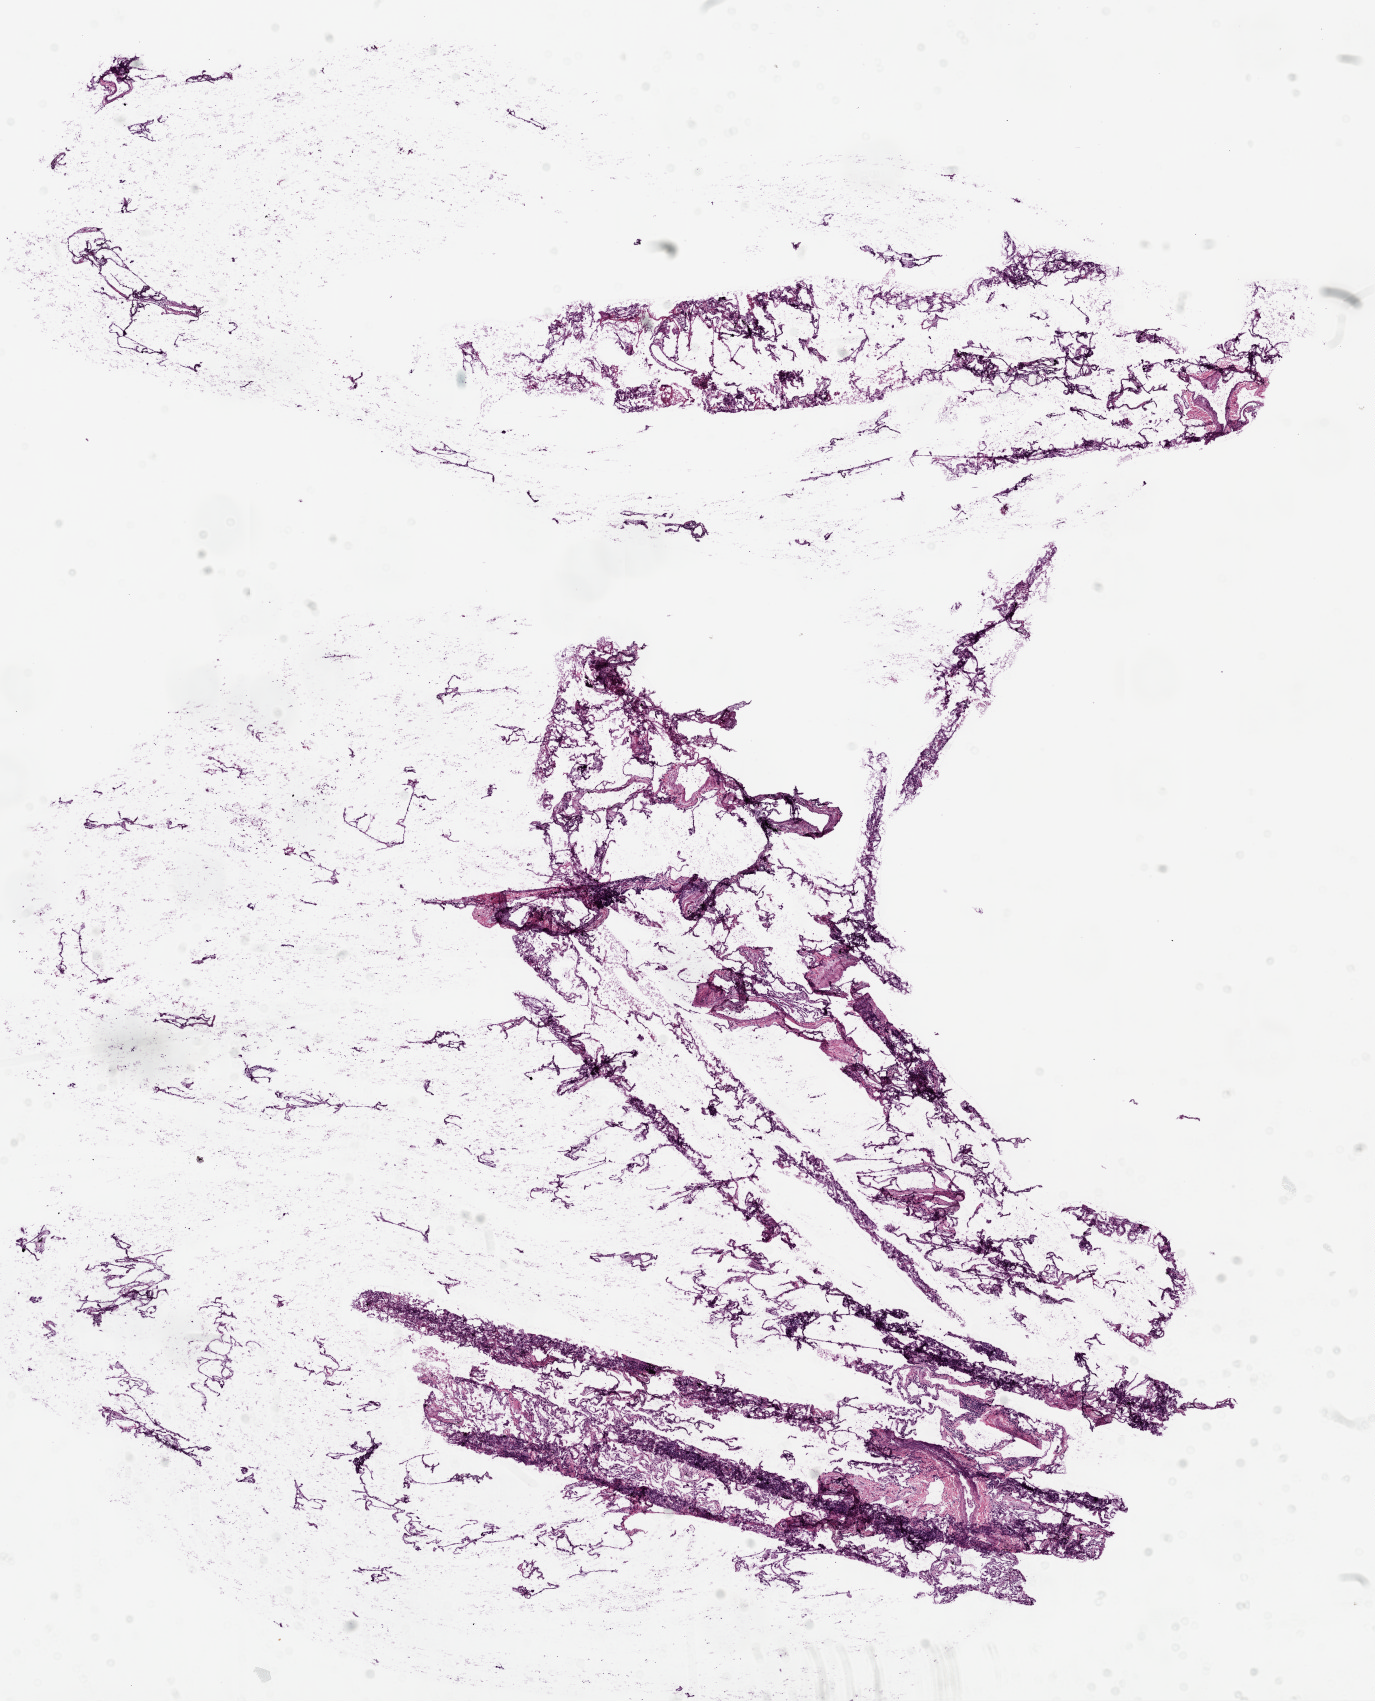
Digitized H&E tissue section (whole slide), low-resolution overview of the scanned area, about 11.0 x 13.6 mm, frozen section from the top of the tissue portion, solid tissue normal (non-tumour tissue) sample from the lung. Female, age 79 years at initial diagnosis.
This section: solid tissue normal (non-tumour) sample from the same patient. Patient diagnosis: Squamous cell carcinoma, NOS (upper lobe, lung).